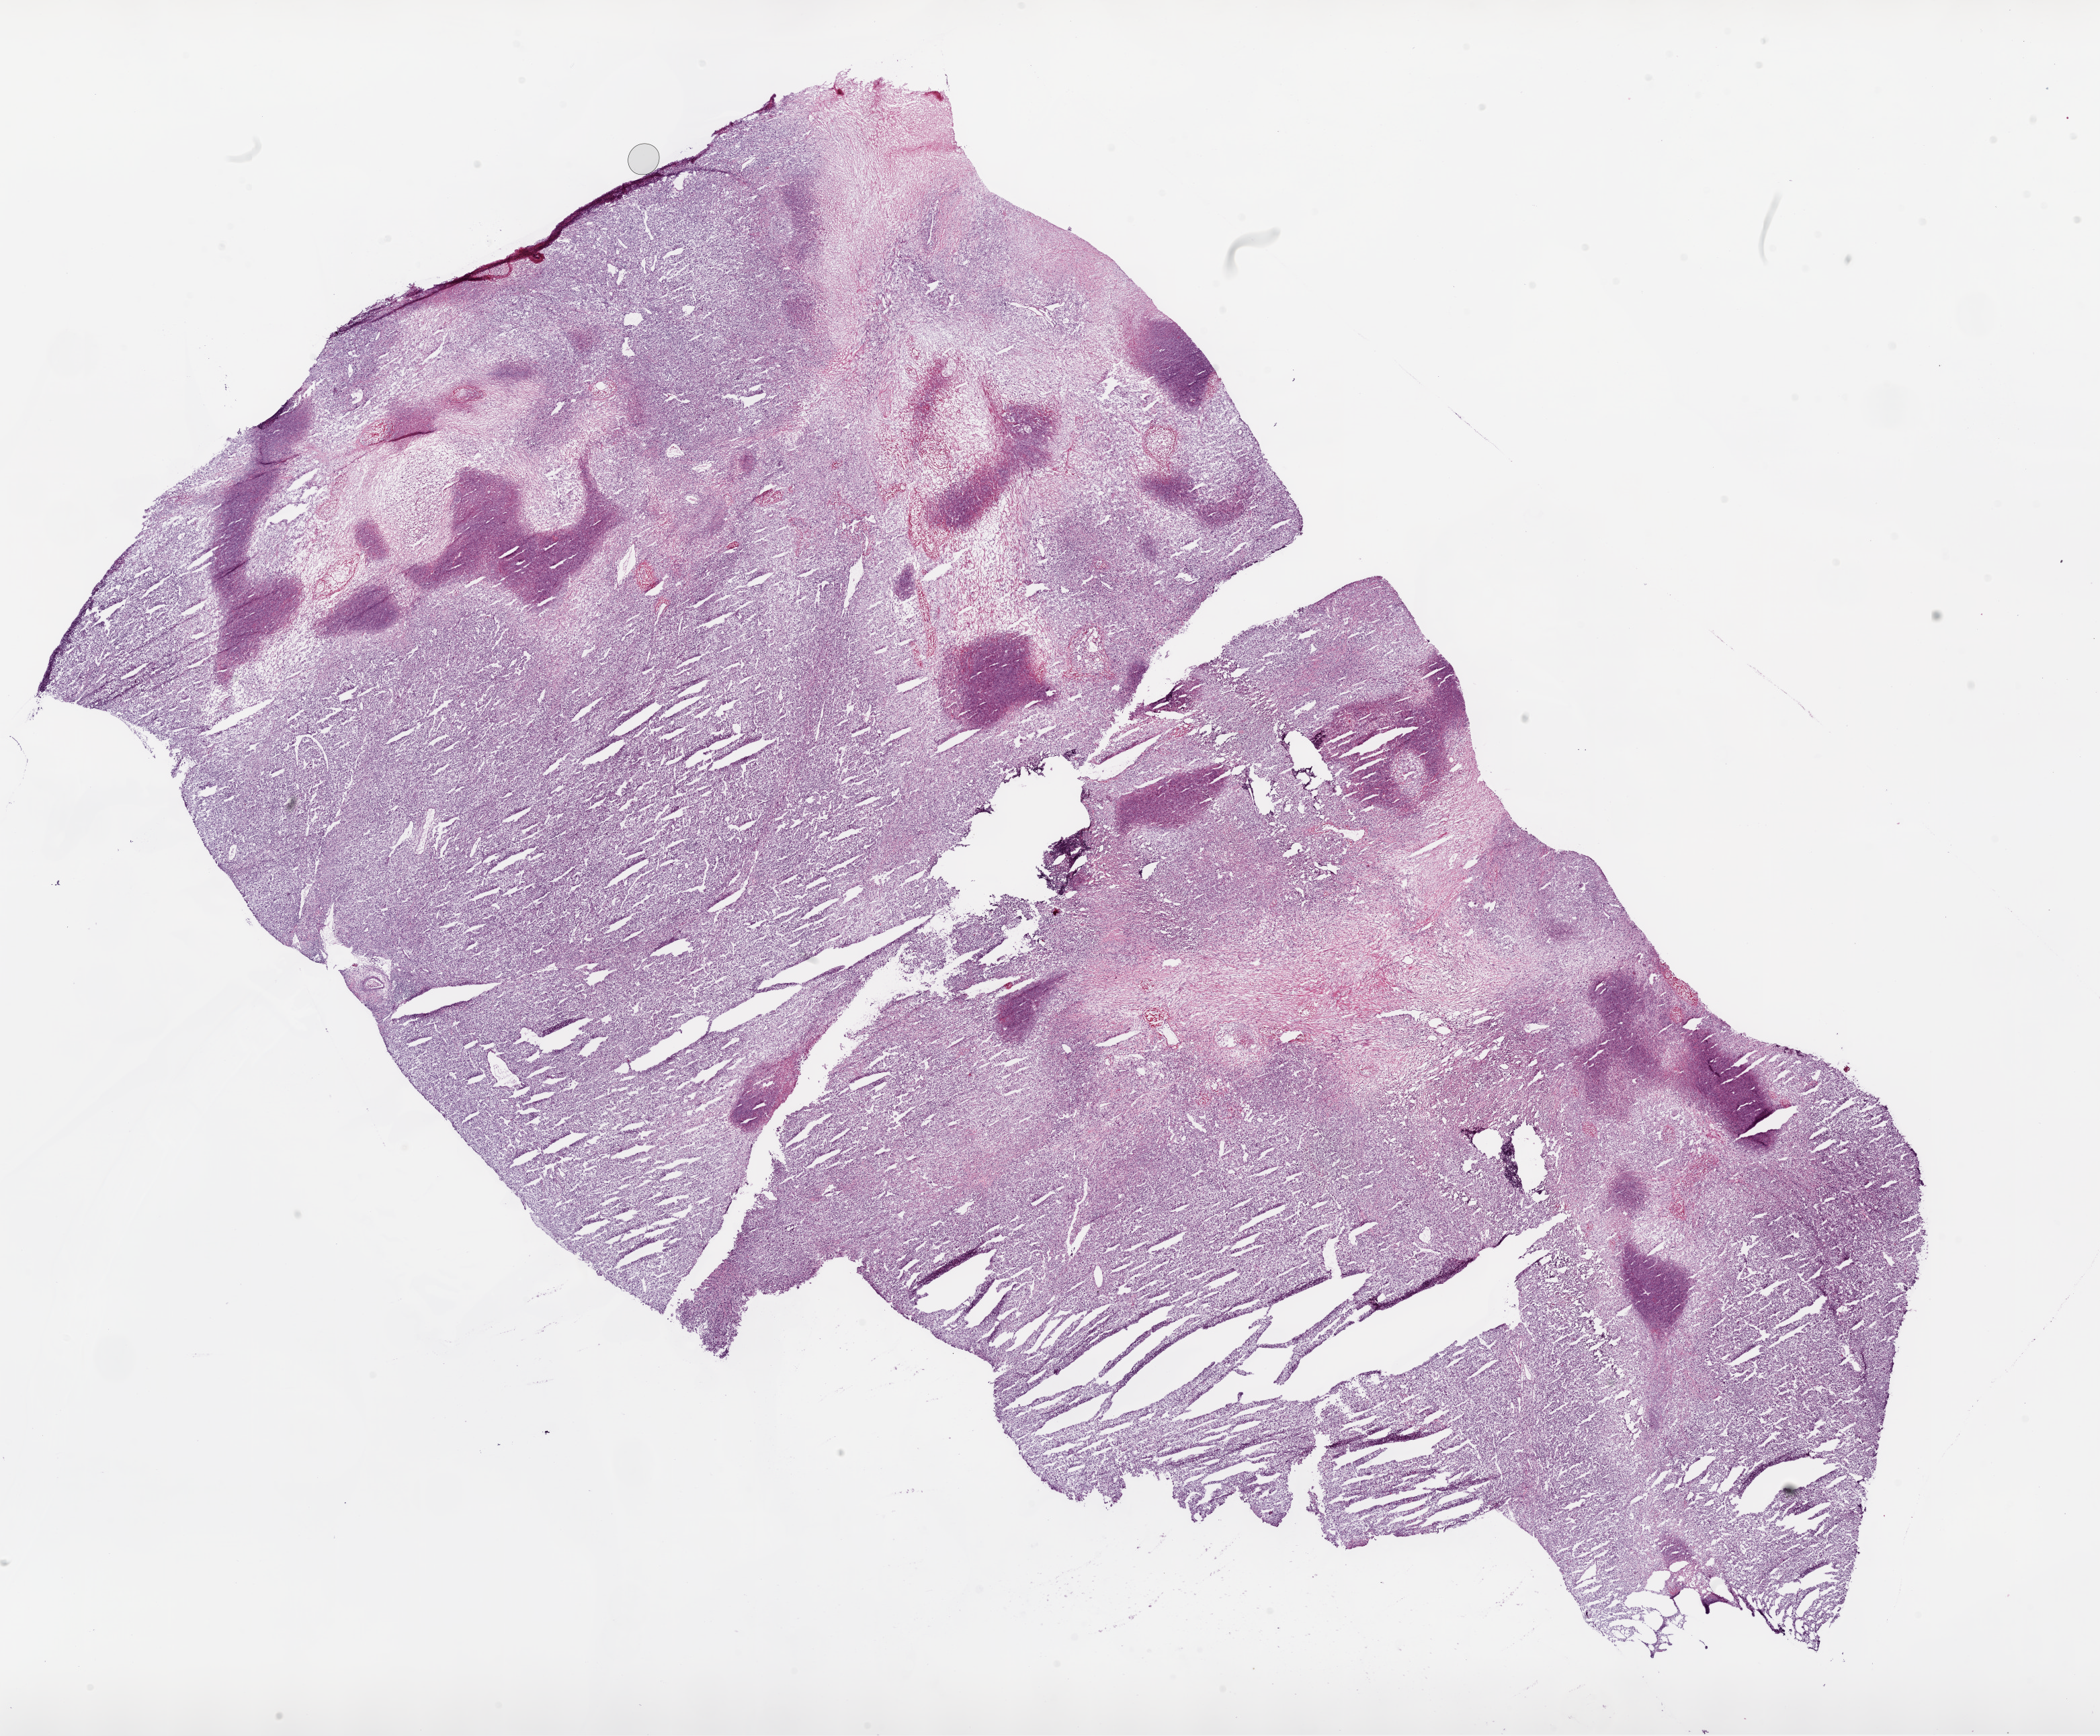
Whole-slide histology image, Hematoxylin and eosin (H&E) stained — shown as a low-resolution overview of the whole scanned area (about 25.1 x 20.7 mm); frozen section; kidney, primary tumour sample. Patient: male, age at initial diagnosis 40 years. Pathologist review of this section (percent, as recorded): tumour cells 75%, tumour nuclei 85%.
Histologic diagnosis: Clear cell adenocarcinoma, NOS.